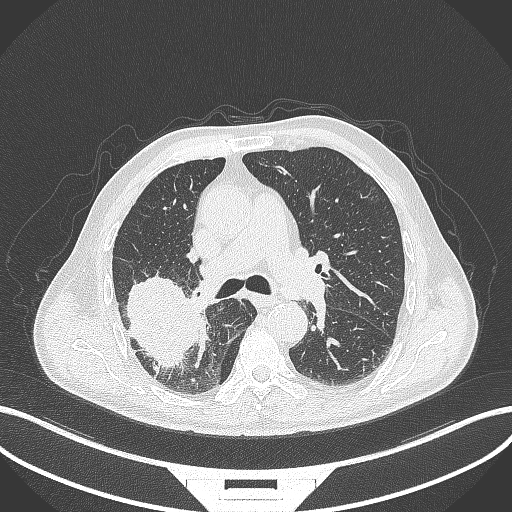
Chest CT, one axial slice. Slice 253 of 429 in the series (ordered by position). Reconstruction kernel B70f. 120 kVp. Lung window (W 1500 / L -600 HU). 1 mm slice thickness. 512 × 512 image matrix, field of view 400 × 400 mm. Patient: male, 72 years. From the clinical record (not read from this slice): clinical TNM (as recorded): T3 N2 M0.
Annotated regions visible in this slice (rectangle marked by the reading radiologist):
- lung tumour (recorded histology: adenocarcinoma): bounding box [x1, y1, x2, y2] px = [122, 276, 207, 373]